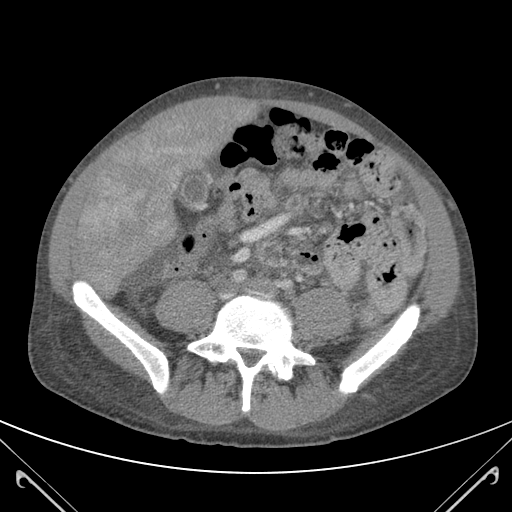
Contrast-enhanced abdominal CT (liver protocol), one axial slice; position 28 of 118 along the scan axis; 120 kVp; soft-tissue window (W 400 / L 40 HU); 3 mm slice thickness; 512 × 512 image matrix, field of view 380 × 380 mm. Case-level facts recorded for this patient, not image findings: diagnosis: hepatocellular carcinoma (patient treated with transarterial chemoembolisation; whether this scan precedes or follows treatment is not stated here); TNM stage (as recorded): Stage-IIIB.
Outlined on this slice (semi-automatic segmentation, software-assisted and operator-edited):
- mass: bounding box (x1, y1, x2, y2) in pixels: (79, 108, 217, 272)